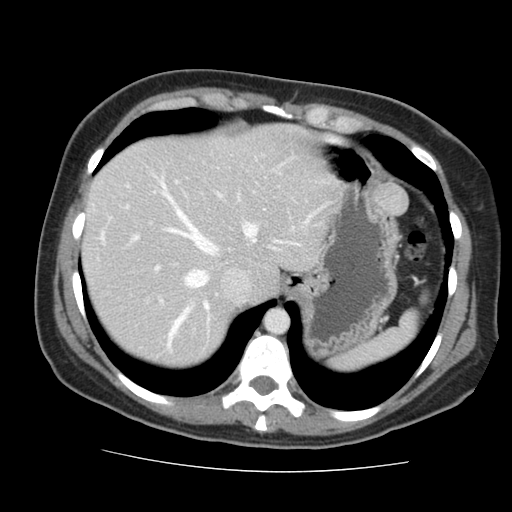
Contrast-enhanced abdominal CT, one axial slice; position 121 of 144 along the scan axis; 120 kVp; intravenous contrast given; soft-tissue window (W 400 / L 40 HU); 2.5 mm slice thickness; 512 × 512 image matrix, field of view 333 × 333 mm. Female patient, age 46 years. Case-level facts recorded for this patient, not image findings: diagnosis: colorectal cancer liver metastases, imaged before liver resection; multiple liver metastases: no; largest metastasis: 2.8 cm; chemotherapy before resection: yes.
Annotated regions visible in this slice (expert manual segmentation):
- hepatic veins: bounding box [x1, y1, x2, y2] px = [159, 178, 331, 341]
- liver: [84, 128, 333, 366]
- planned liver remnant (the part of the liver to remain after resection): [84, 128, 333, 366]
- portal vein (with intrahepatic branches): [102, 182, 220, 345]